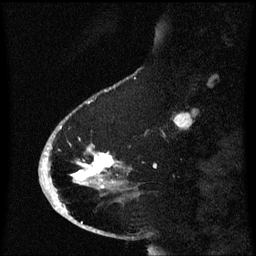
Breast MRI (dynamic contrast-enhanced), one sagittal slice. Slice 18 of 60 in the series (ordered by position). Dynamic contrast-enhanced series, image 2 of 3 at this slice position (ordered by acquisition). 1.5 T. TE 4.2 ms, TR 8.4 ms. 2.1 mm slice thickness. 256 × 256 image matrix, field of view 200 × 200 mm. Patient: female, 53 years. From the clinical record (not read from this slice): setting: breast cancer imaged before/during neoadjuvant chemotherapy; receptor status: HR-positive, HER2-negative.
Annotated regions visible in this slice (semi-automatic segmentation, software-assisted and operator-edited):
- analysis volume of interest (the breast-tissue region the enhancement analysis was run in; not a lesion): bounding box (x1, y1, x2, y2) in pixels: (49, 108, 131, 201)
- tumour enhancement mask (voxels above the 70 % enhancement threshold inside the analysis volume of interest): (75, 154, 115, 181)